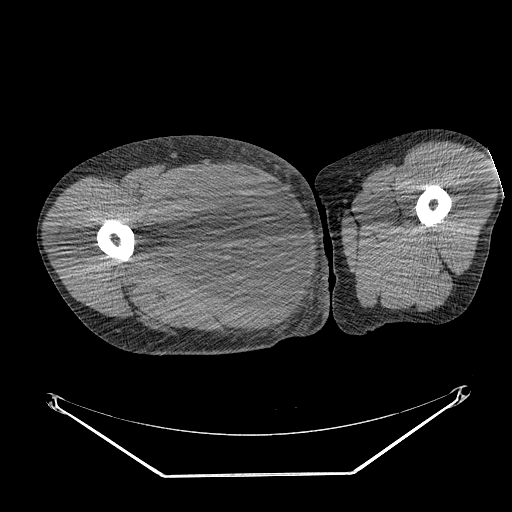
CT of an extremity soft-tissue mass (from a PET/CT study), one axial slice; position 259 of 311 along the scan axis; reconstruction kernel STANDARD; soft-tissue window (W 400 / L 40 HU); 3.75 mm slice thickness; 512 × 512 image matrix. Male patient. Case-level facts recorded for this patient, not image findings: histological type: undifferentiated - pleiomorphic; grade: high; site of the primary tumour: right thigh.
Outlined on this slice (expert contour drawn on MRI and transferred to this co-registered scan by the dataset authors):
- gross tumour volume including surrounding oedema: bounding box <142,167,266,279> (left, top, right, bottom; pixels)
- gross tumour volume (mass): <153,169,266,275>